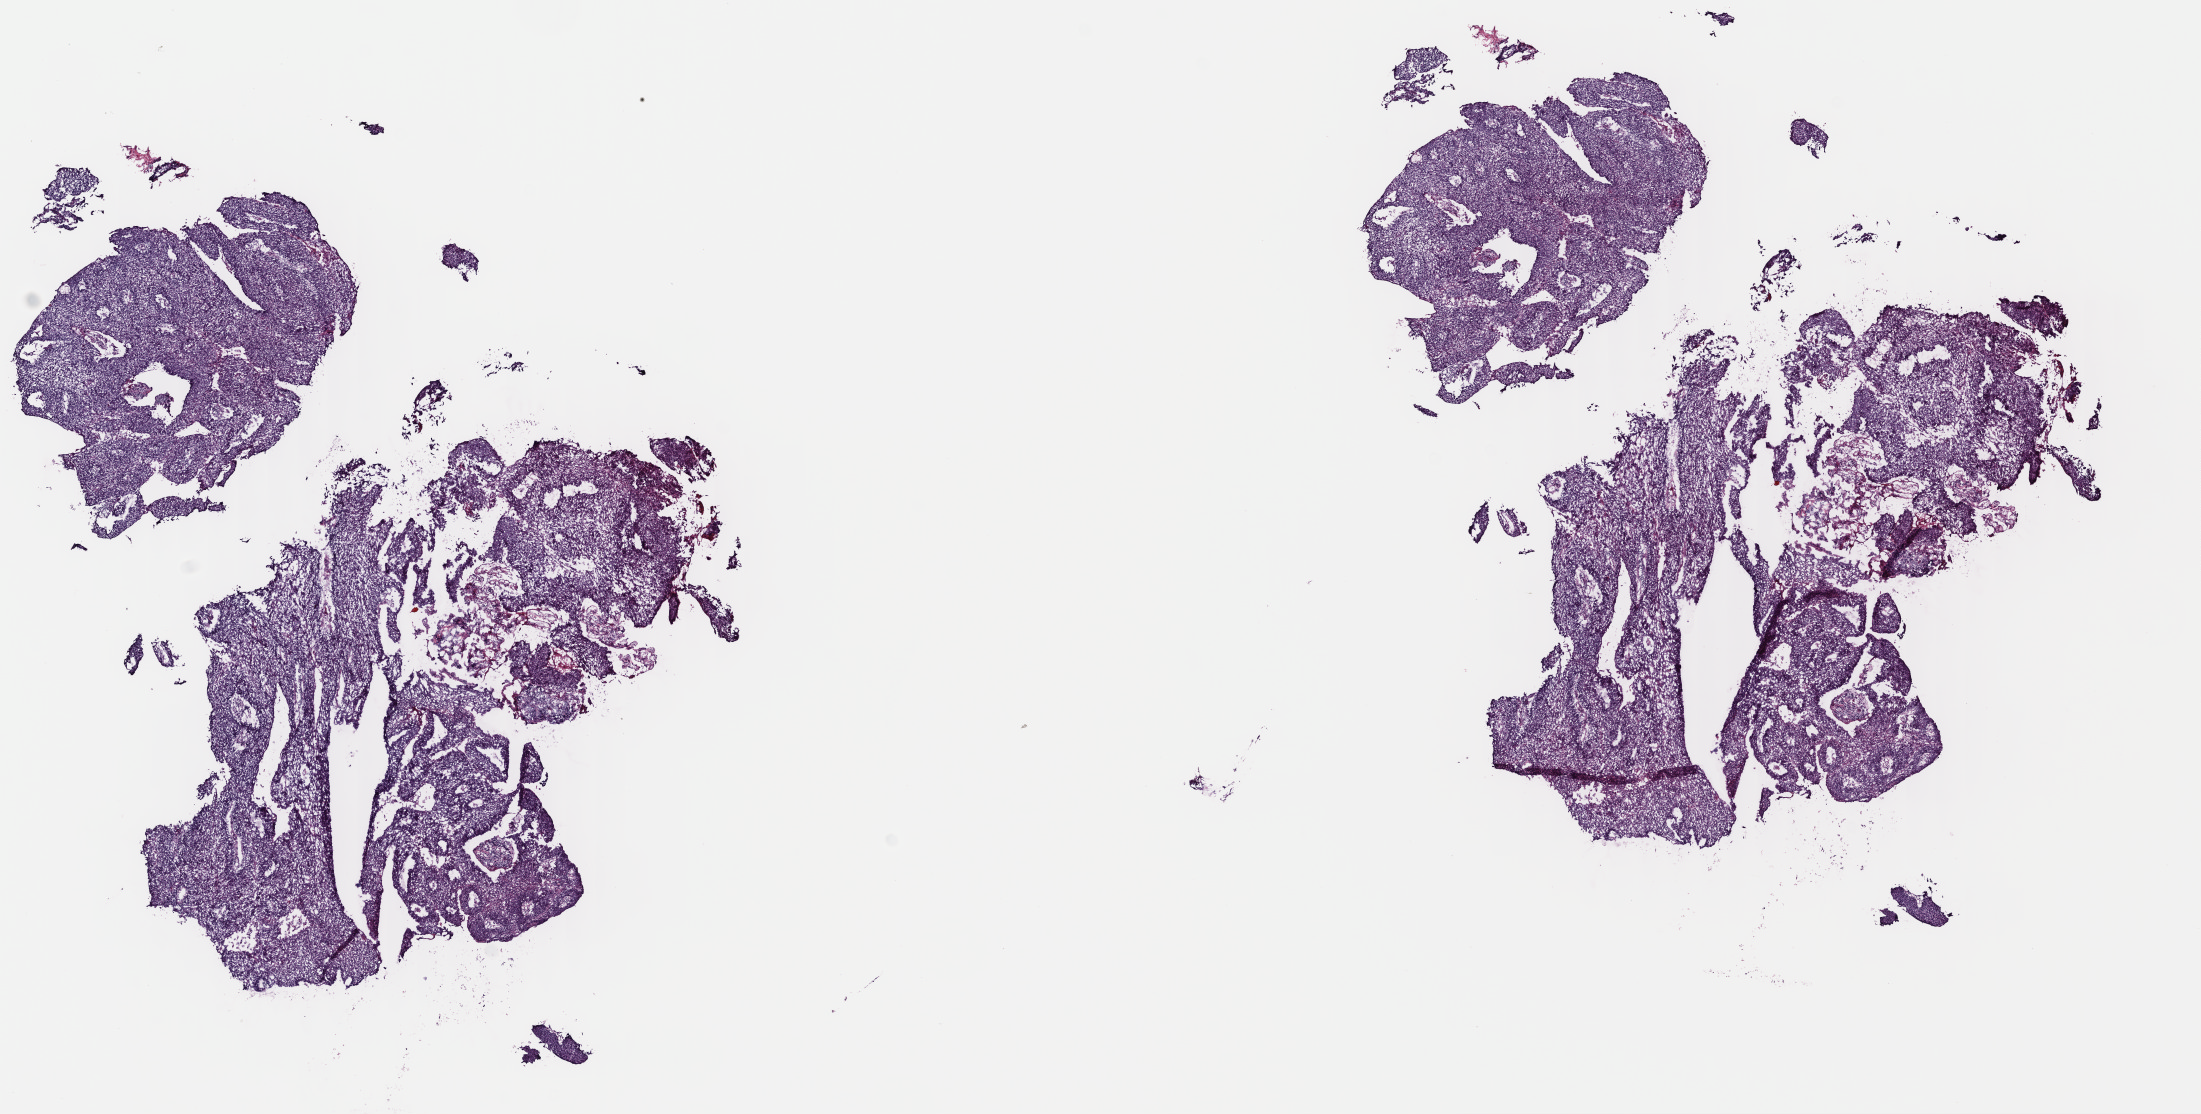
Digitized H&E-stained tissue section (whole slide), a low-resolution overview of the entire scanned area, about 17.3 x 8.8 mm (acquisition: 40x scan); frozen section; sample: primary tumour, head and neck. Male, age 40 years at initial diagnosis. Histologic grade: GX (grade cannot be assessed). Slide review estimates, as recorded: tumour cells 75%, tumour nuclei 75%, normal cells 0%, stromal cells 24%, necrosis 1%. Inflammatory infiltration, as recorded: lymphocyte infiltration 3%, monocyte infiltration 2%, neutrophil infiltration 5%.
- laterality: right
- AJCC pathologic stage: IVA (7th edition)
- TNM: T2 N2b MX
- diagnosis: Squamous cell carcinoma, large cell, nonkeratinizing, NOS